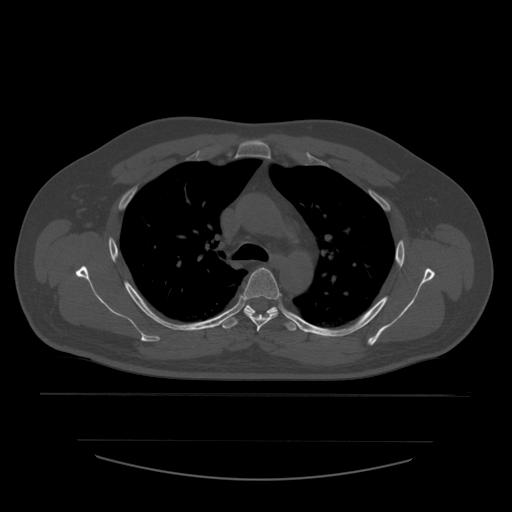
CT including the spine, one axial slice. Slice 411 of 532 in the series (ordered by position). Reconstruction kernel STANDARD. 120 kVp. Bone window (W 1800 / L 400 HU). 1.25 mm slice thickness. 512 × 512 image matrix, field of view 441 × 441 mm. Patient age 44 years. From the clinical record (not read from this slice): primary cancer: soft tissue sarcoma.
Structures marked on this image (semi-automatic segmentation, software-assisted and operator-edited):
- T4 vertebra: box from (x=242, y=268) to (x=282, y=332) px
- T5 vertebra: (x=220, y=305)–(x=297, y=331)